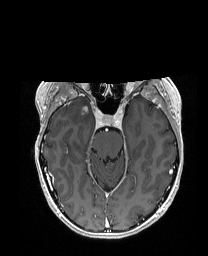
Brain MRI from a brain-tumour surgery series, one axial slice; position 117 of 192 along the scan axis; T1-weighted post-contrast; 1 mm slice thickness; 208 × 256 image matrix, field of view 203 × 250 mm. Case-level facts recorded for this patient, not image findings: histopathology: Metastatic Carcinoma from Breast primary; tumour location: Right Frontal.
Annotated regions visible in this slice (manually delineated by an expert):
- tumour: bounding box <97,105,101,110> (left, top, right, bottom; pixels)